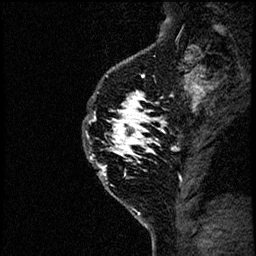
Breast MRI (dynamic contrast-enhanced), one sagittal slice; position 50 of 60 along the scan axis; dynamic contrast-enhanced study with each time point stored as its own series, time point 2 of 4 at this slice position (early post-contrast, ordered by acquisition time); 1.5 T; TE 4.2 ms, TR 17.6 ms; 2 mm slice thickness; 256 × 256 image matrix. Female patient, age 40 years. Case-level facts recorded for this patient, not image findings: setting: breast cancer imaged before/during neoadjuvant chemotherapy; receptor status: HER2-positive.
Structures marked on this image (semi-automatically segmented with operator editing):
- analysis volume of interest (the breast-tissue region the enhancement analysis was run in; not a lesion): box from (x=78, y=55) to (x=185, y=206) px
- tumour enhancement mask (voxels above the 100 % enhancement threshold inside the analysis volume of interest): (x=82, y=87)–(x=185, y=183)